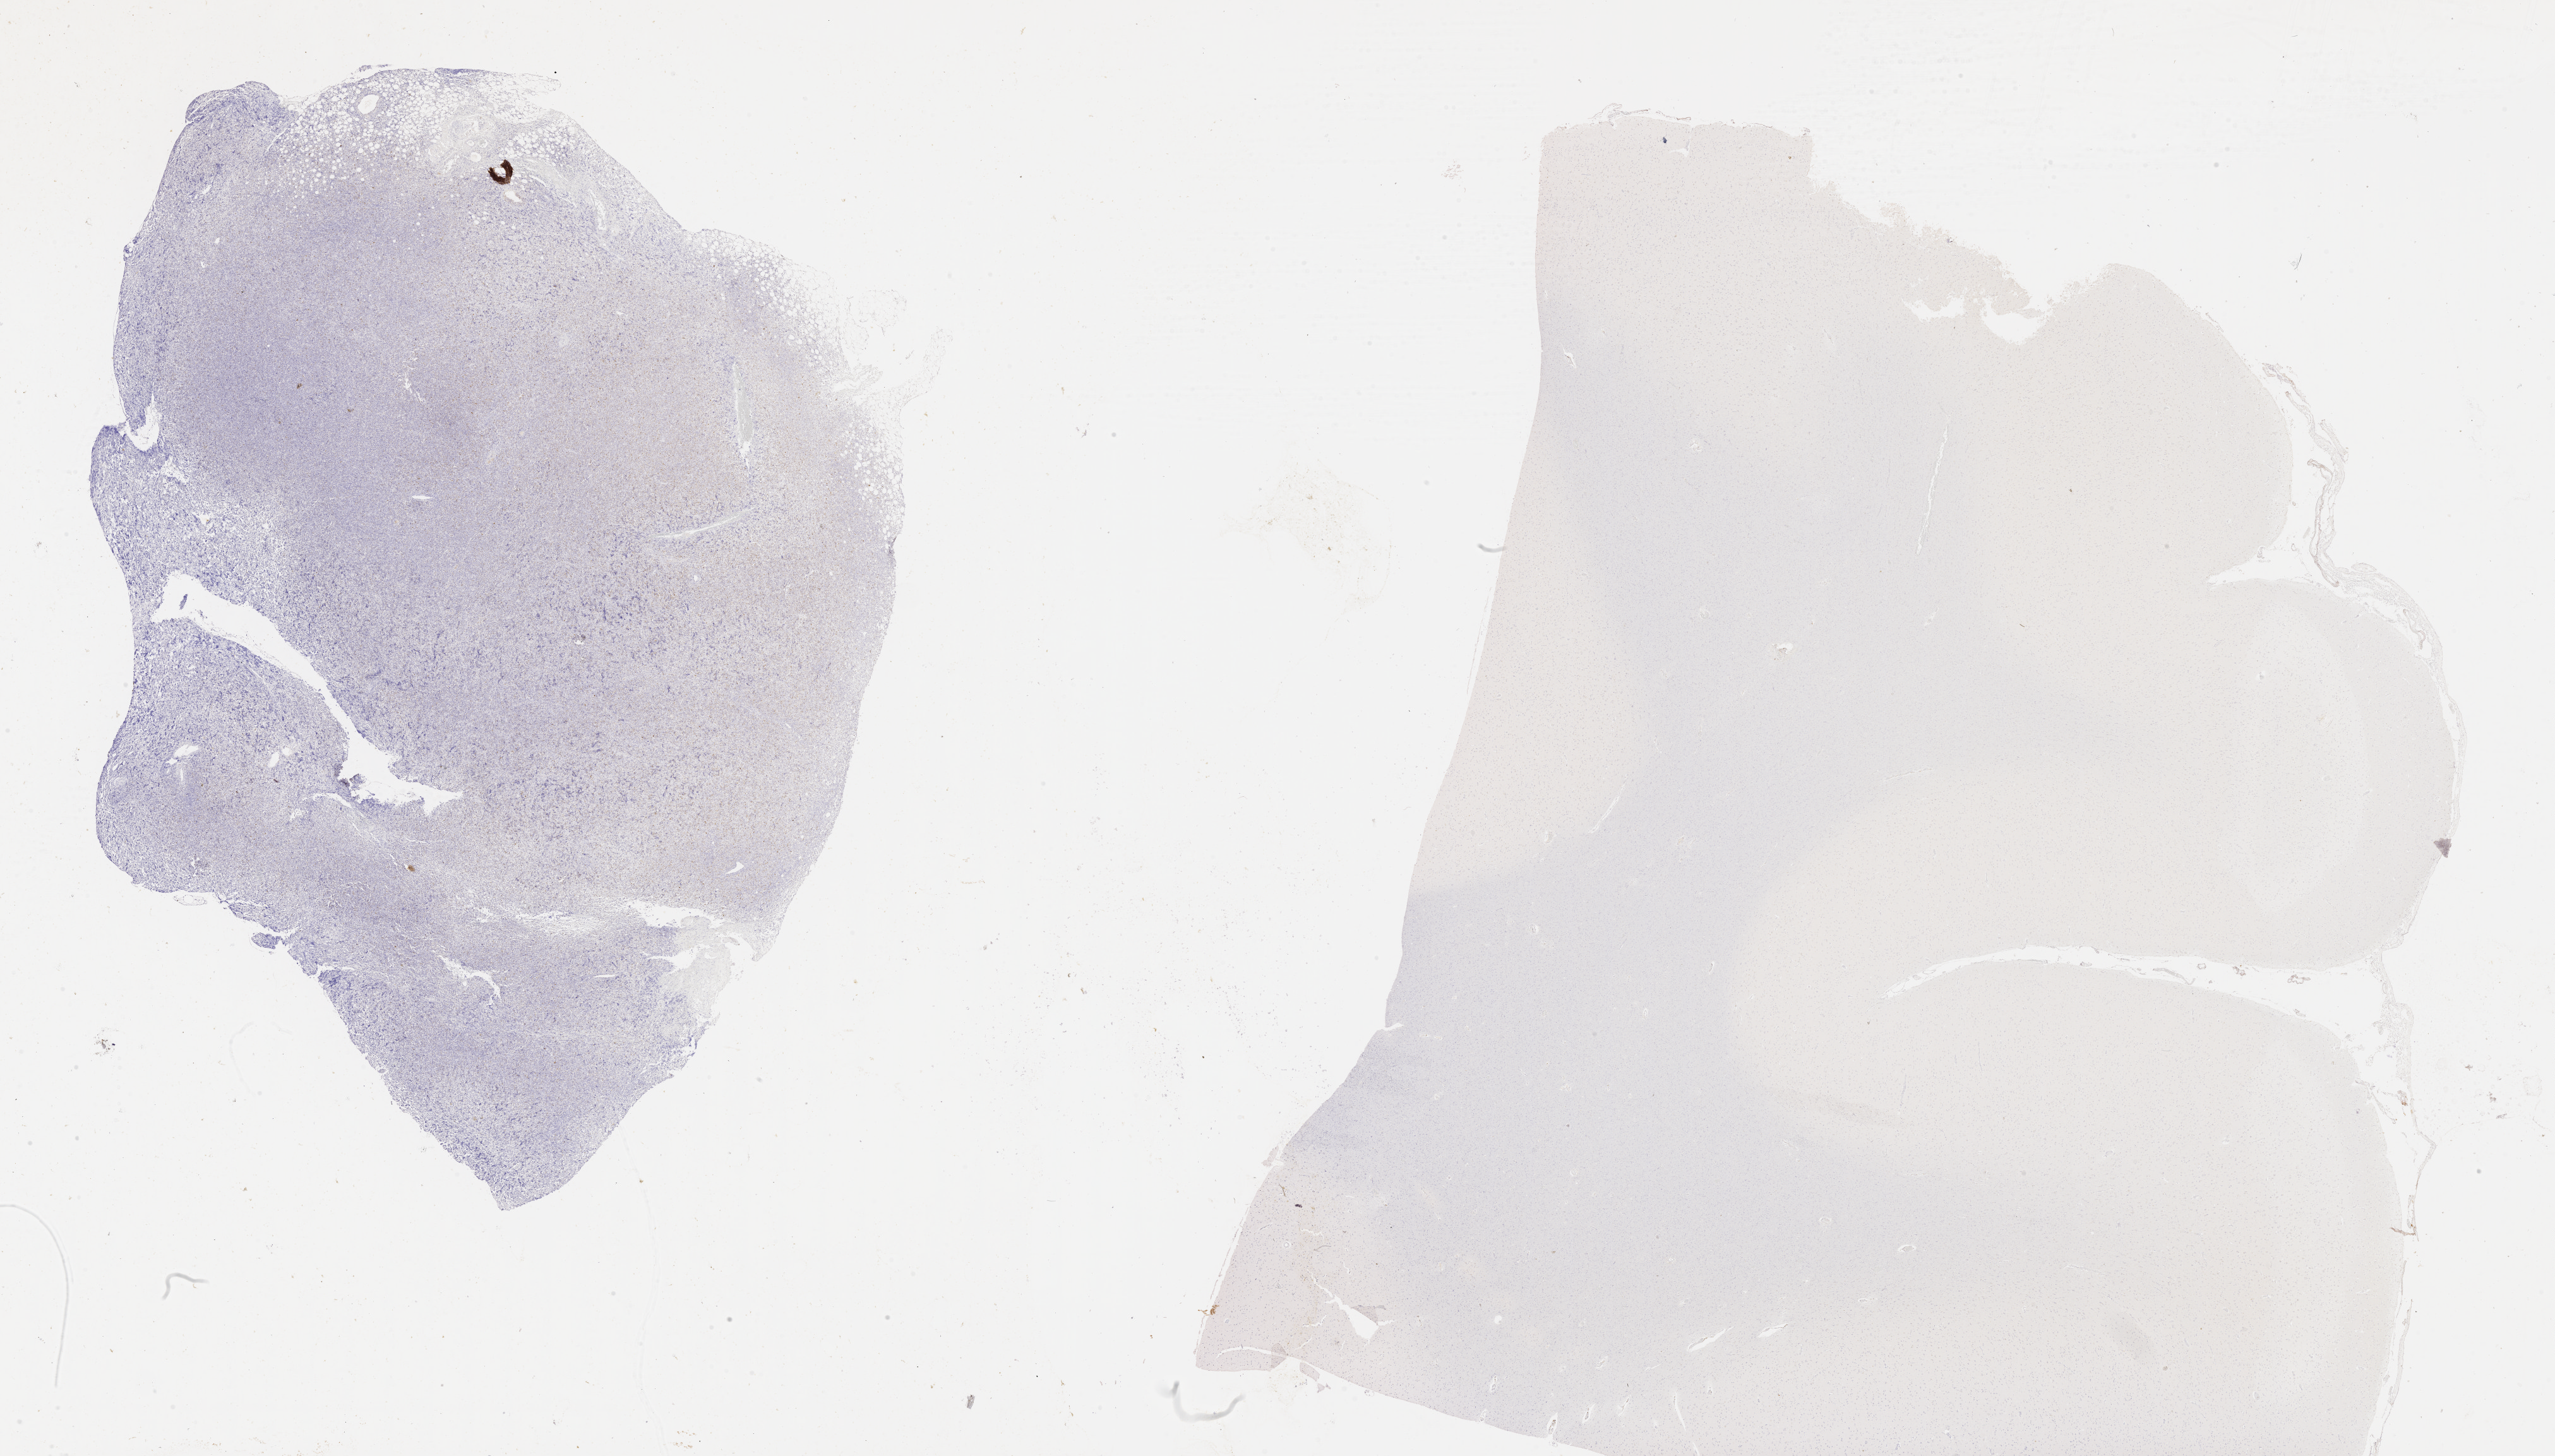
Whole-slide image, immunohistochemical stain for p53, whole scanned area (about 32.7 x 18.6 mm) shown as a low-resolution overview. Female patient.
Specimen: tumor tissue.